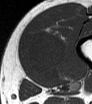
MRI of an extremity soft-tissue mass, one axial slice; position 16 of 62 along the scan axis; MR volume resampled by the dataset authors to the PET/CT grid (not the native acquisition matrix); 3.27 mm slice thickness; 92 × 104 image matrix, field of view 90 × 102 mm. Male patient. Case-level facts recorded for this patient, not image findings: histological type: mixoid liposarcoma; grade: low; site of the primary tumour: left thigh.
Structures marked on this image (expert contour drawn on MRI and transferred to this co-registered scan by the dataset authors):
- gross tumour volume (mass): bounding box (x1, y1, x2, y2) in pixels: (25, 33, 67, 82)